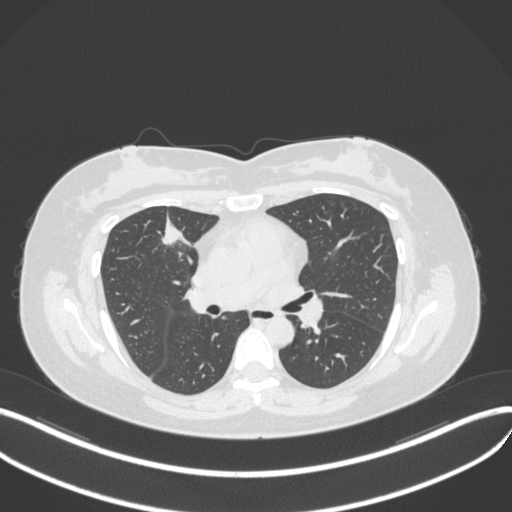
Chest CT, one axial slice; position 179 of 272 along the scan axis; reconstruction kernel B31f; 120 kVp; lung window (W 1500 / L -600 HU); 1 mm slice thickness; 512 × 512 image matrix, field of view 400 × 400 mm. Female patient, age 42 years. Case-level facts recorded for this patient, not image findings: clinical TNM (as recorded): T1b N0 M0.
Outlined on this slice (rectangle marked by the reading radiologist):
- lung tumour (recorded histology: adenocarcinoma): bounding box [x1, y1, x2, y2] px = [156, 210, 190, 253]